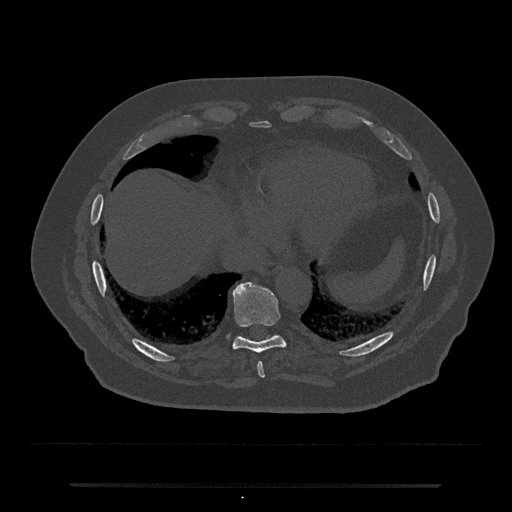
CT including the spine, one axial slice. Position 753 of 797 along the scan axis. Reconstruction kernel Br40s/3. 120 kVp. Bone window (W 1800 / L 400 HU). 0.5 mm slice thickness. 512 × 512 image matrix, field of view 434 × 434 mm. Patient: male, 80 years. Case-level facts recorded for this patient, not image findings: primary cancer: prostate; vertebrae with lytic lesions (as recorded): L1, T11.
Outlined on this slice (semi-automatically segmented with operator editing):
- T10 vertebra: box from (x=239, y=334) to (x=277, y=338) px
- T8 vertebra: (x=257, y=362)–(x=265, y=378)
- T9 vertebra: (x=231, y=281)–(x=285, y=353)